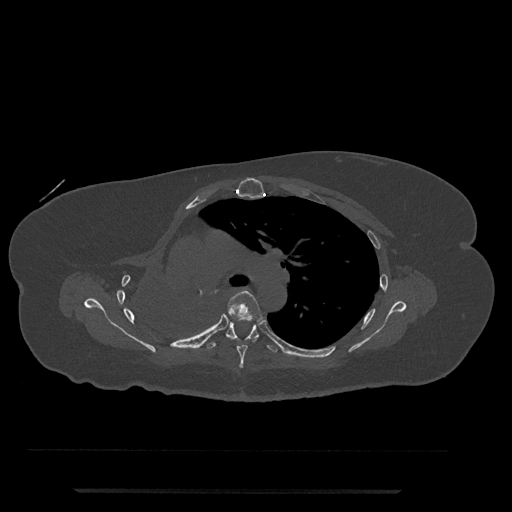
CT including the spine, one axial slice; slice 520 of 797 in the series (ordered by position); reconstruction kernel Br40s/3; bone window (W 1800 / L 400 HU); 512 × 512 image matrix, field of view 440 × 440 mm. Female patient, age 51 years. From the clinical record (not read from this slice): primary cancer: neuro.
Outlined on this slice (semi-automatic segmentation, software-assisted and operator-edited):
- T5 vertebra: bounding box <228,290,263,369> (left, top, right, bottom; pixels)
- T6 vertebra: <206,322,278,353>